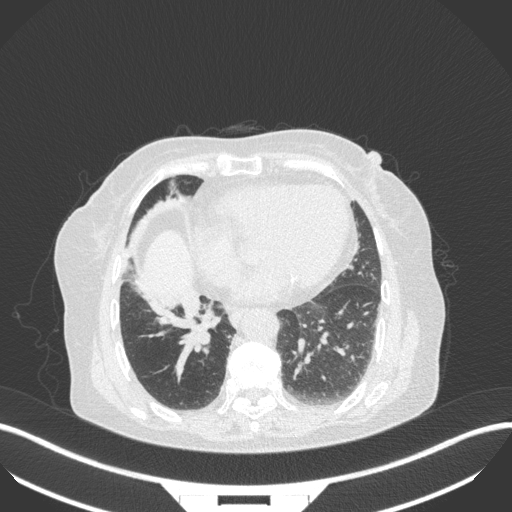
Chest CT, one axial slice; slice 112 of 329 in the series (ordered by position); 120 kVp; lung window (W 1500 / L -600 HU); 512 × 512 image matrix, field of view 400 × 400 mm. Female patient, age 75 years. From the clinical record (not read from this slice): clinical TNM (as recorded): T1b N0 M1a.
Structures marked on this image (bounding box drawn by a radiologist):
- lung tumour (recorded histology: squamous cell carcinoma): box from (x=179, y=296) to (x=218, y=349) px